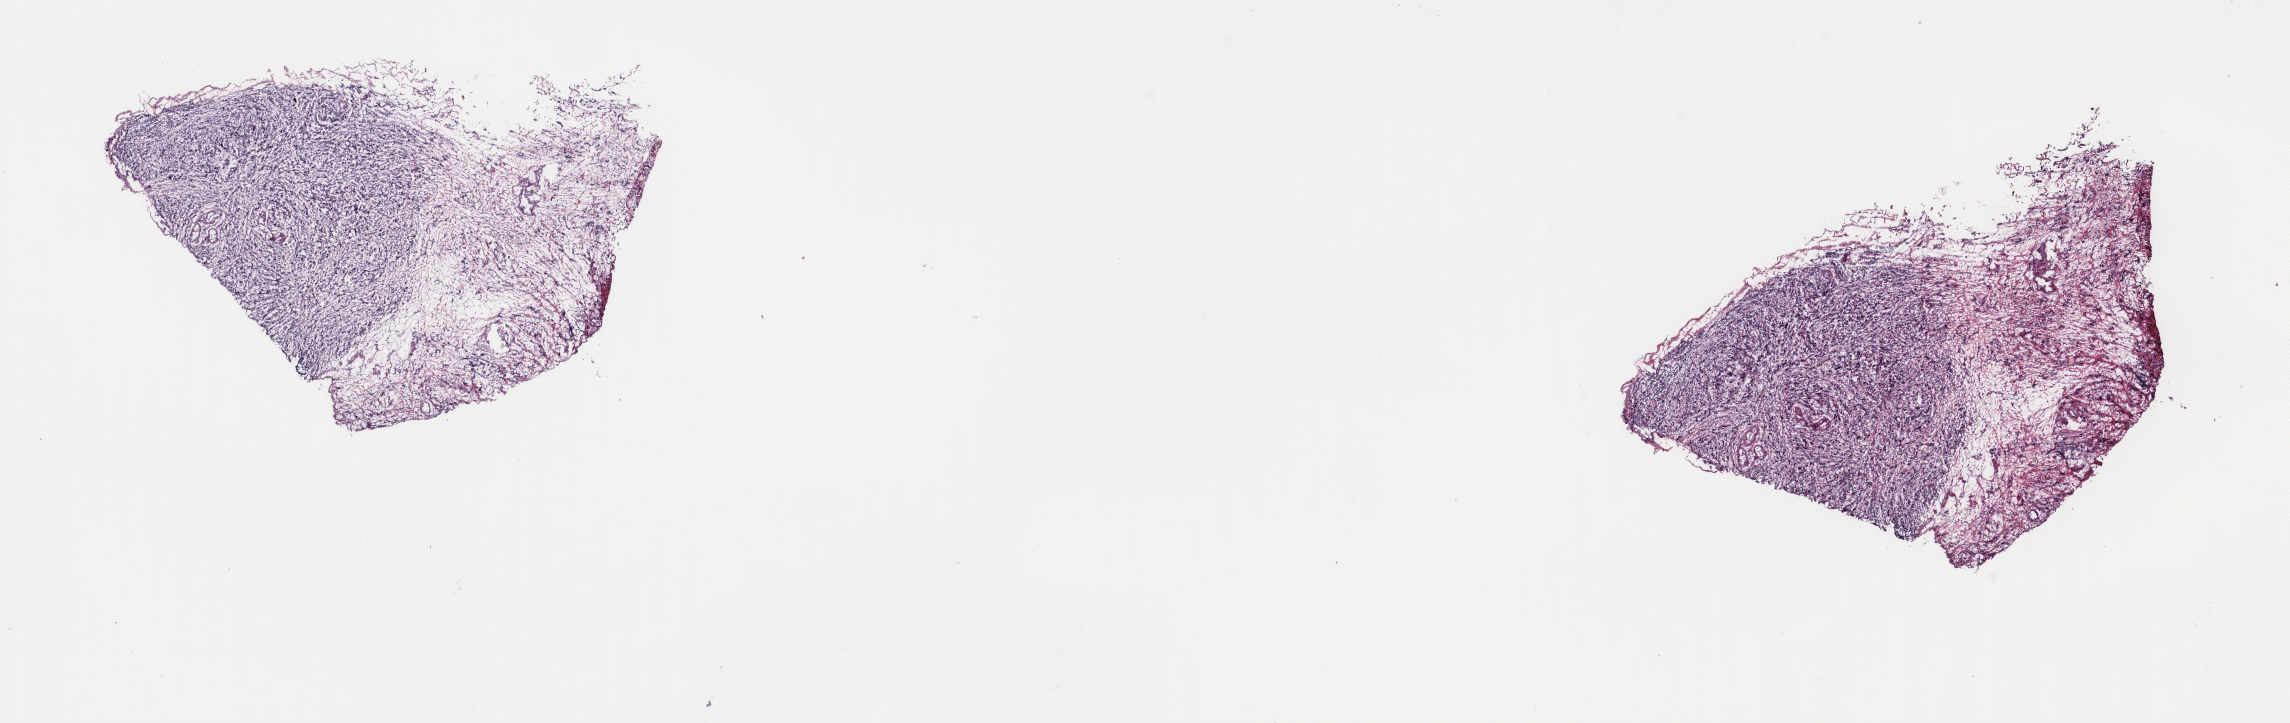
Digitized Hematoxylin and eosin (H&E) stained tissue section (whole slide), a low-resolution overview of the entire scanned area, about 18.2 x 5.7 mm. Frozen section. Sample: primary tumour, stomach. Female, age 76 years at initial diagnosis.
Diagnosis: Carcinoma, diffuse type (gastric antrum).